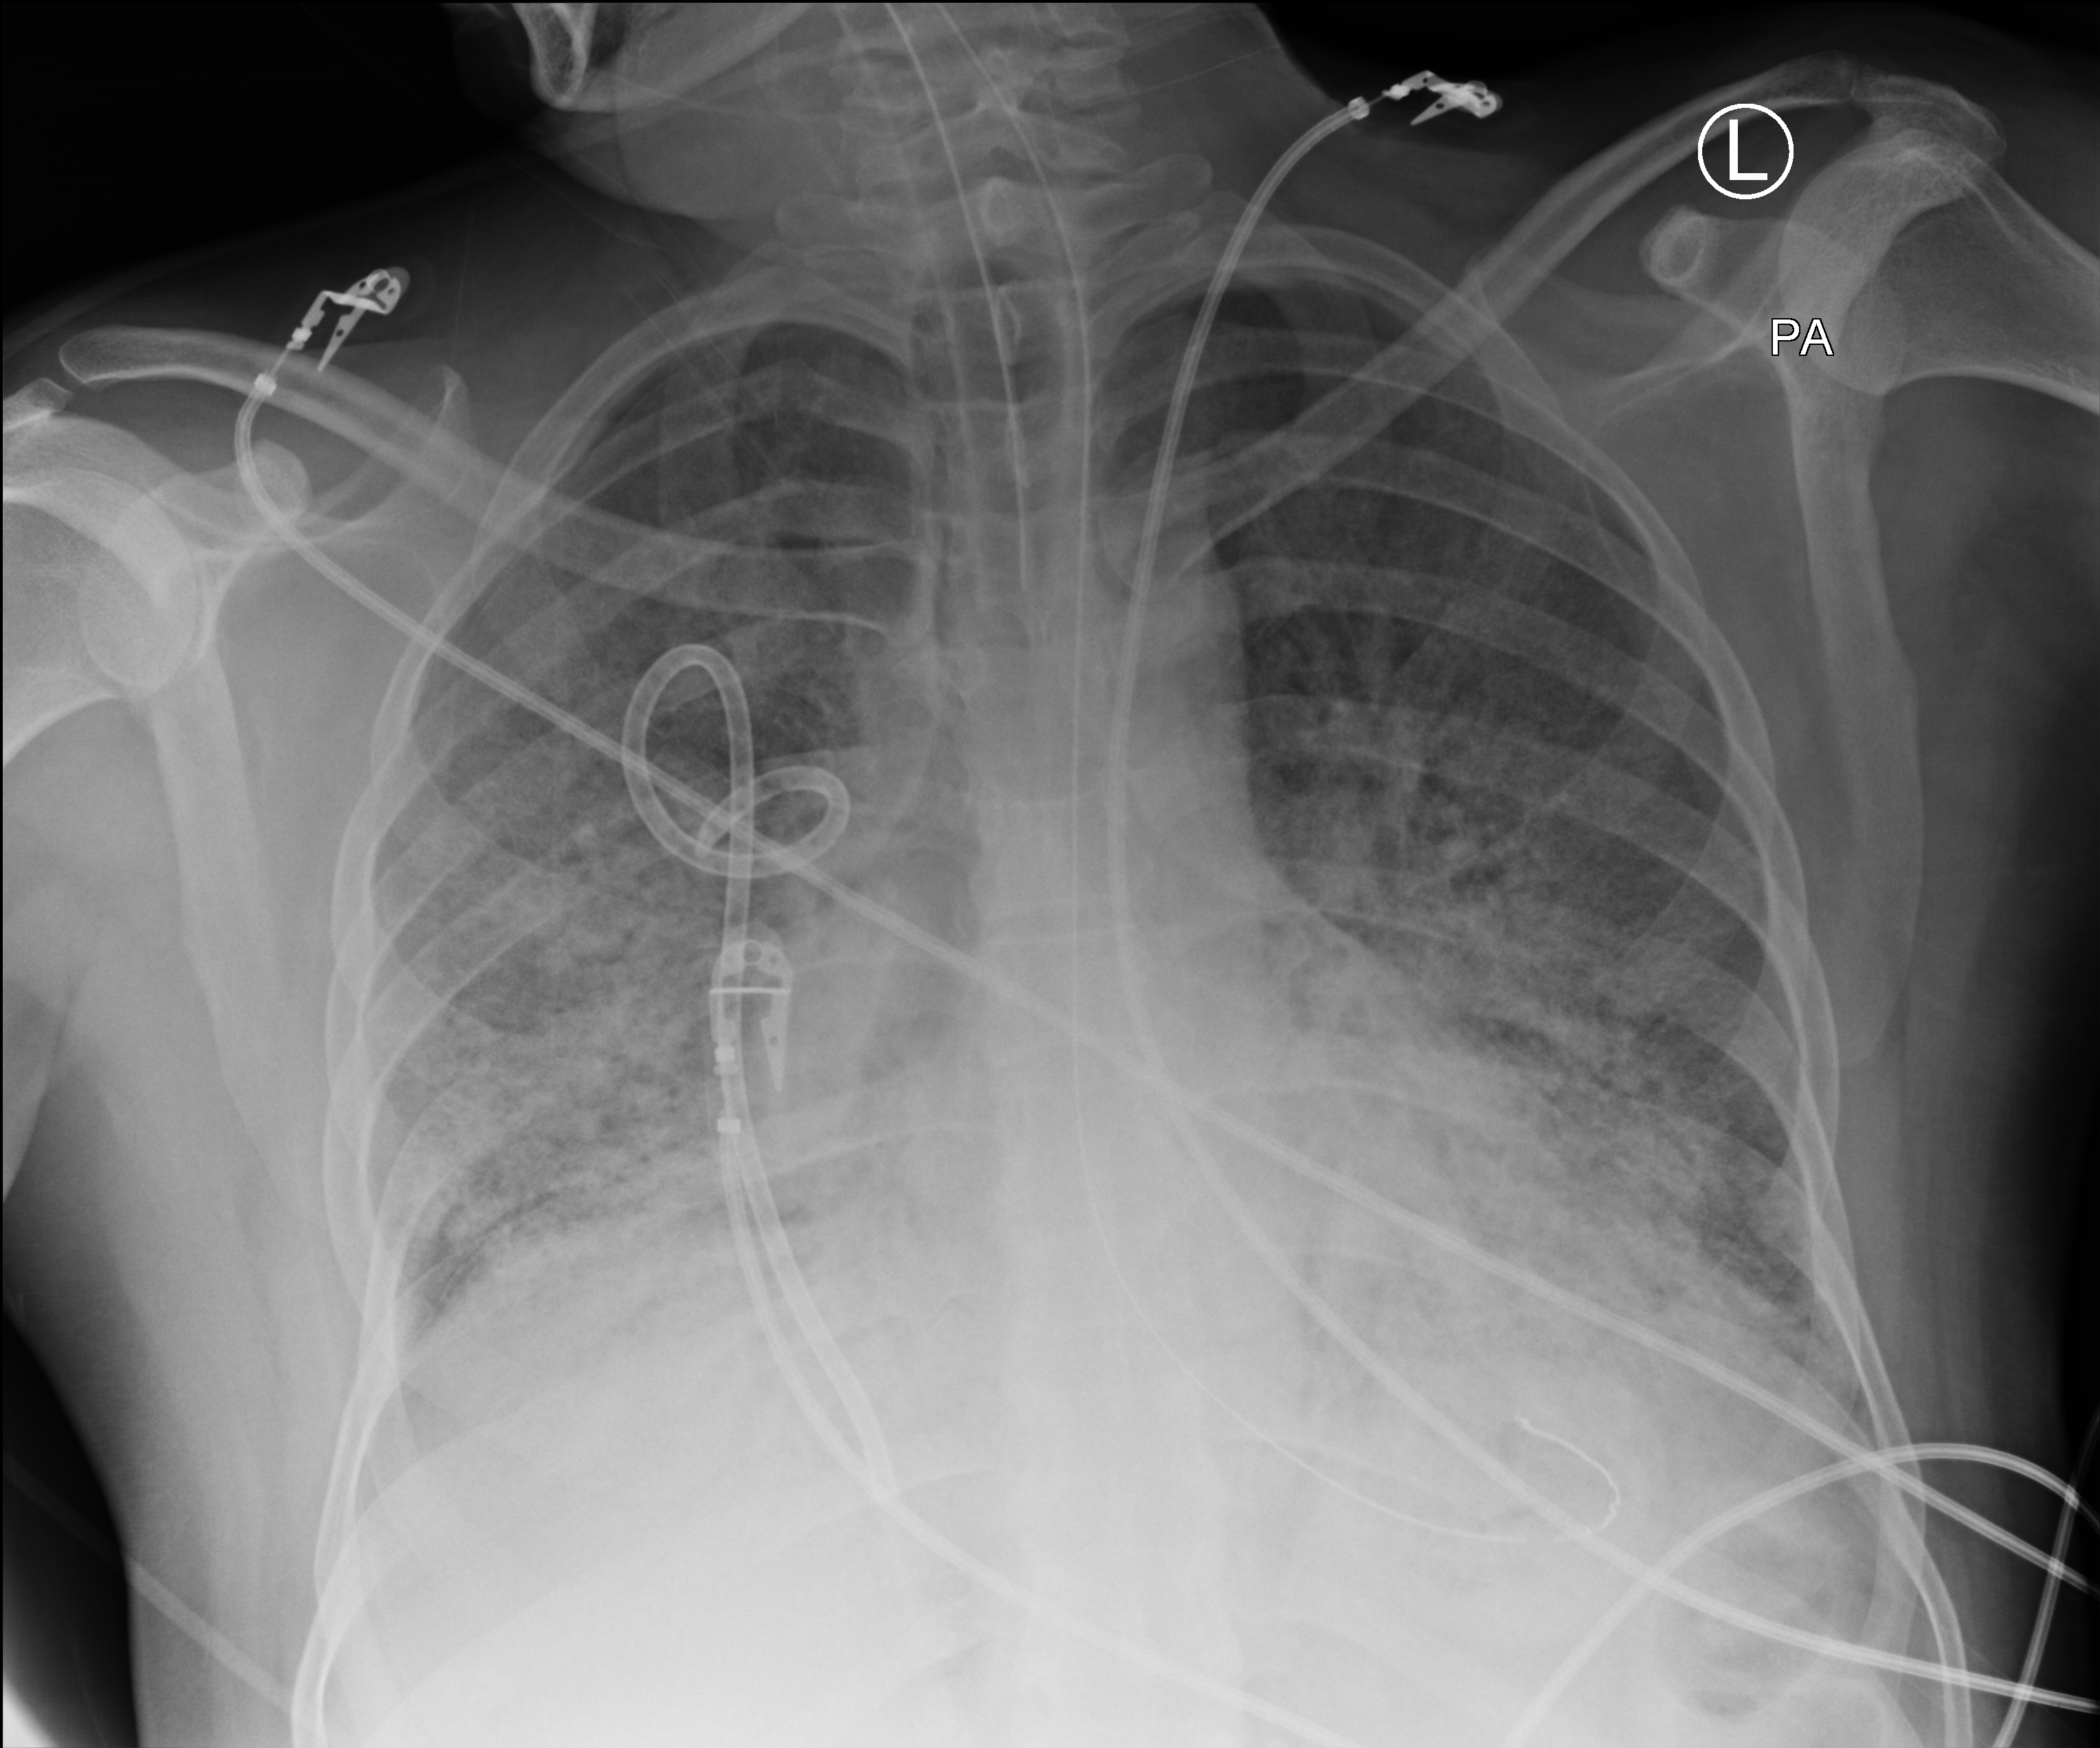
Portable chest radiograph; posteroanterior (PA) projection. Patient hospitalised with COVID-19, aged 18–59 years.
Hospital-stay facts (about this admission, not read from this image; timing relative to this image not recorded):
- smoking status (admission record): never
- admitted to intensive care during this hospital stay: yes